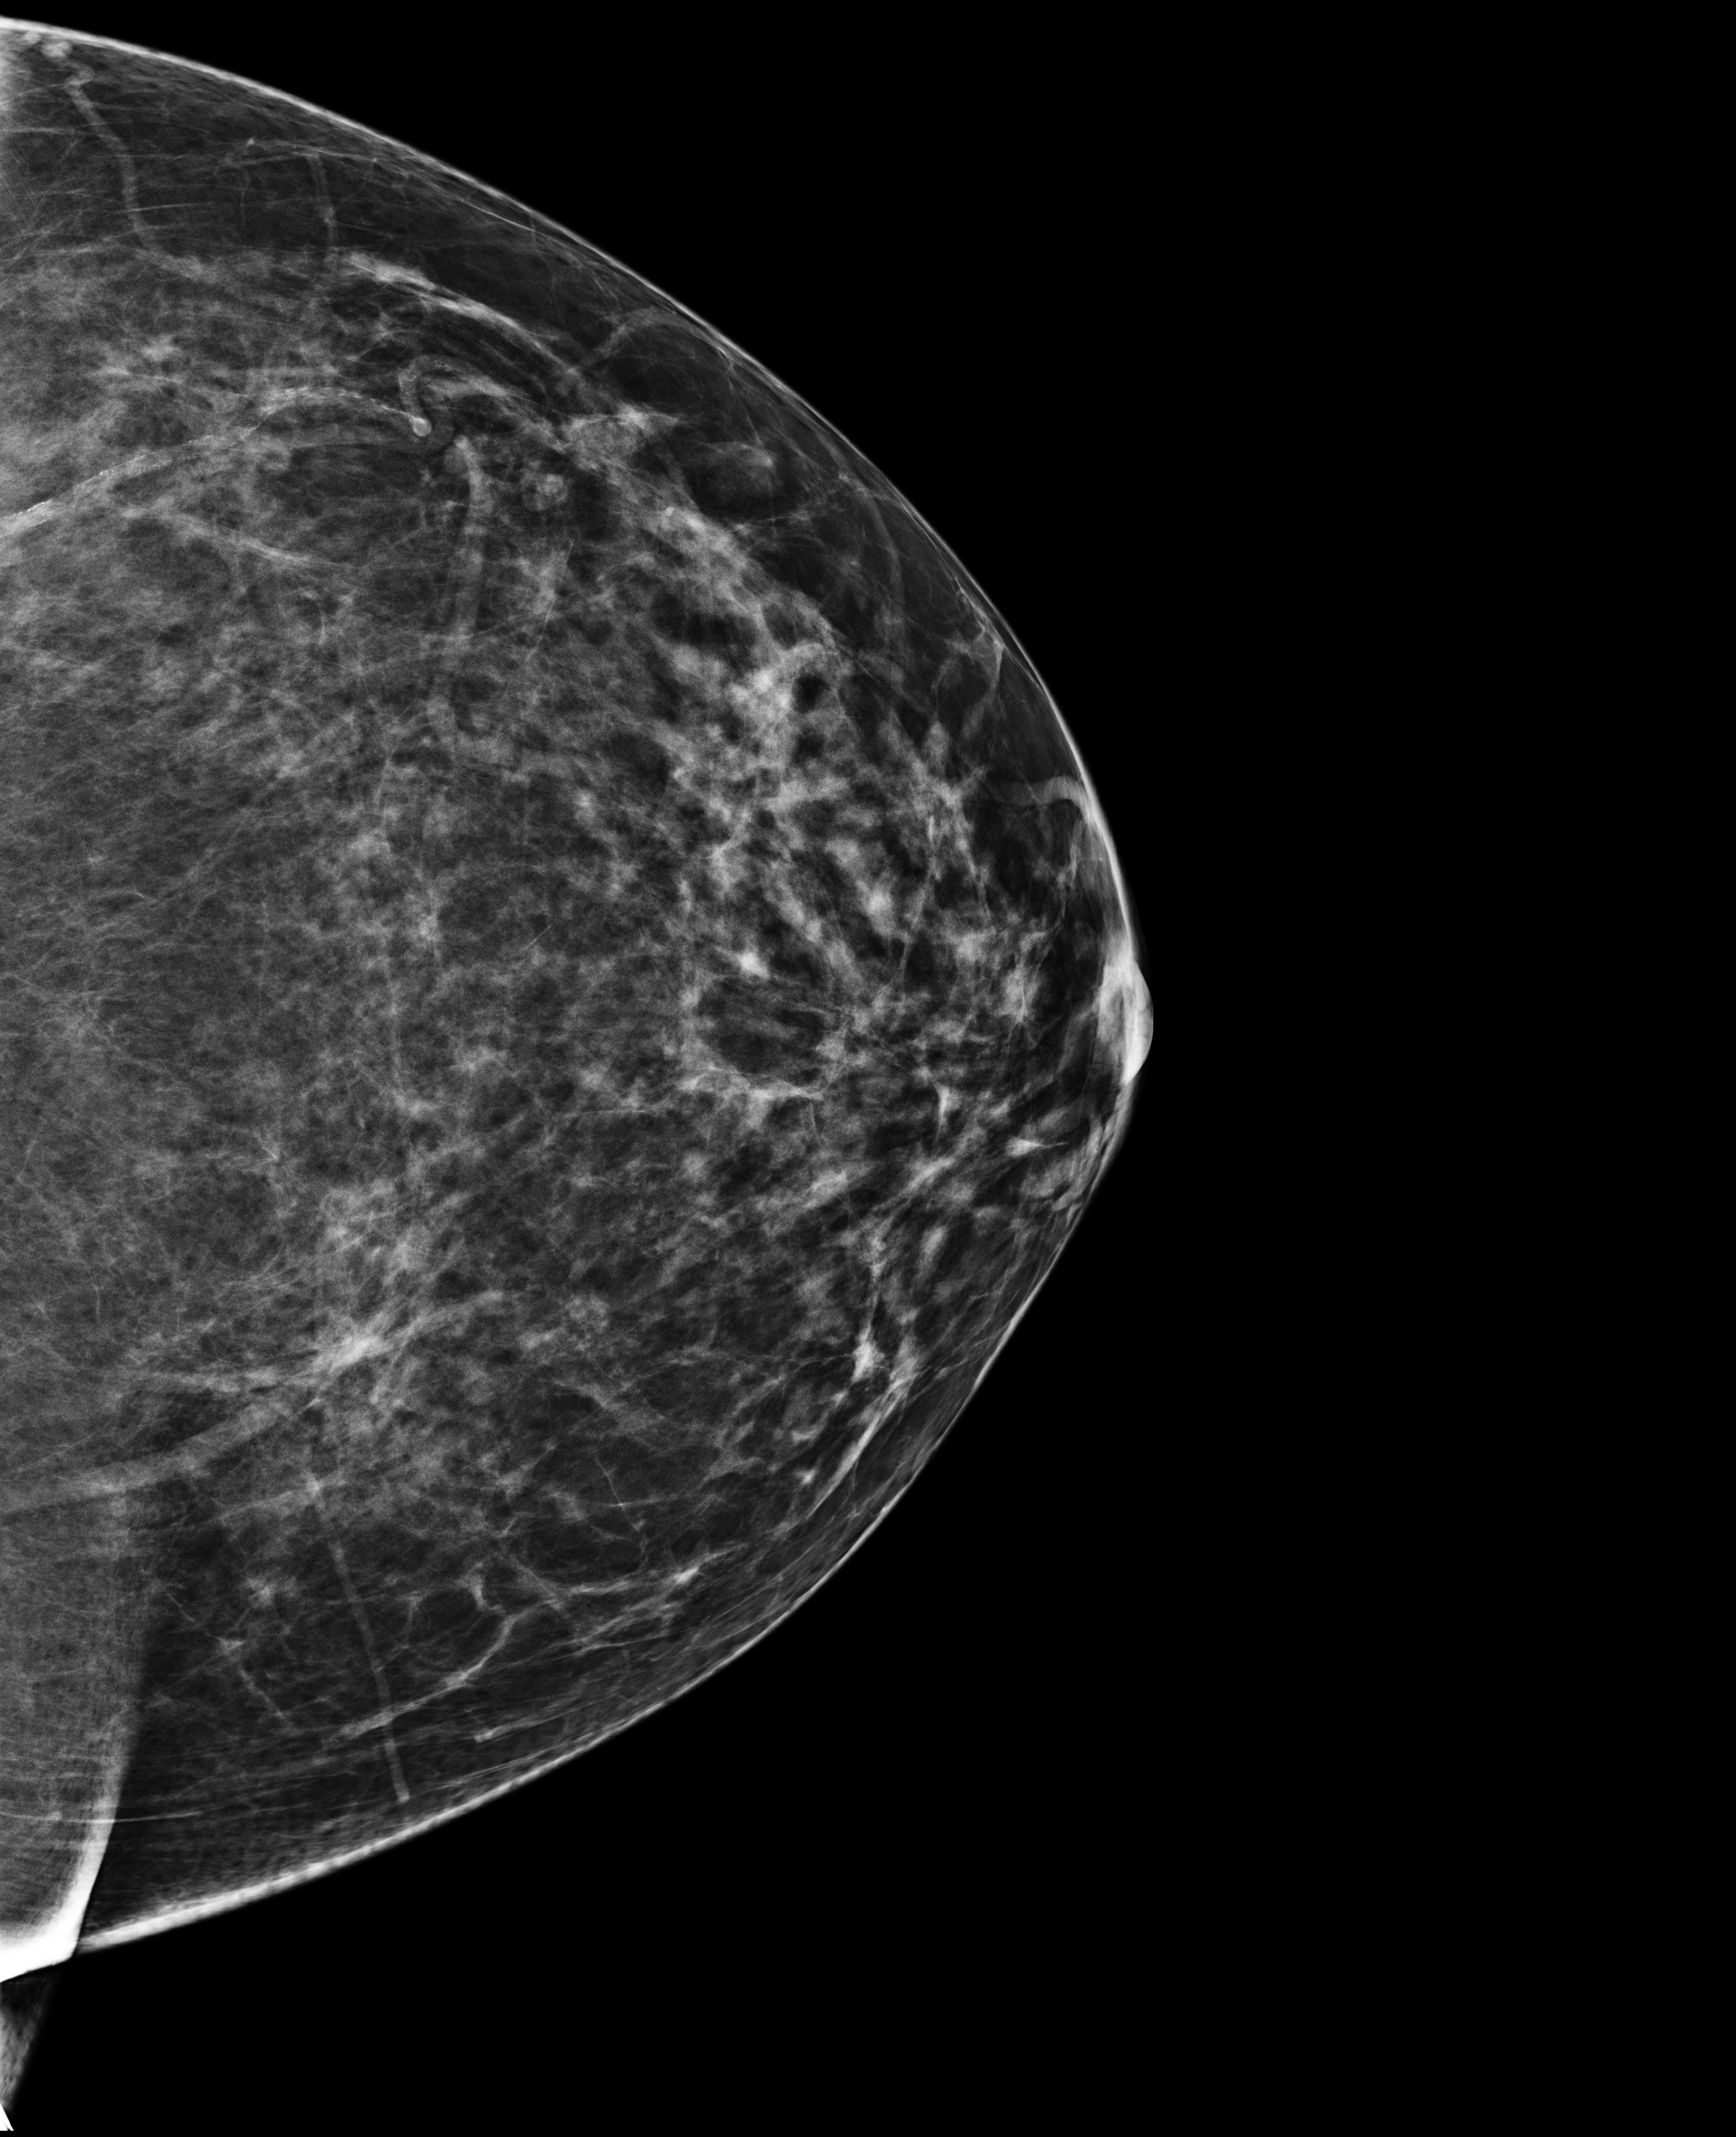
Full-field digital mammogram (FFDM), left breast, cranio-caudal projection, annual screening mammography examination, compressed breast thickness 79 mm. Patient: female, 67 years.
Breast density at the screening exam (both breasts): scattered fibroglandular densities (BI-RADS density category b). Final BI-RADS assessment for this screening round (tomosynthesis exam, both breasts): category 1. Recall: no recall after this screen.